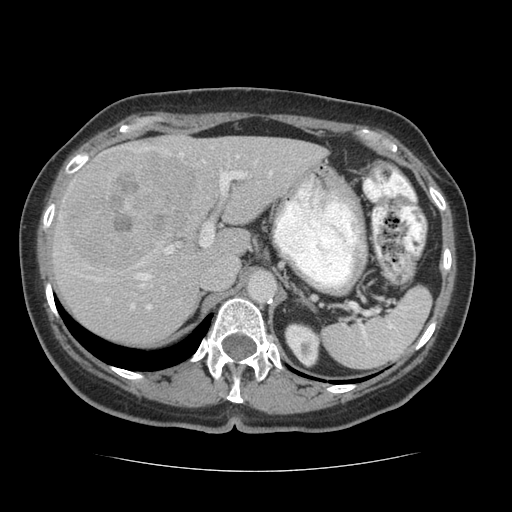
Contrast-enhanced abdominal CT (liver protocol), one axial slice; position 42 of 75 along the scan axis; 140 kVp; soft-tissue window (W 400 / L 40 HU); 2.5 mm slice thickness; 512 × 512 image matrix, field of view 360 × 360 mm. Case-level facts recorded for this patient, not image findings: diagnosis: hepatocellular carcinoma (patient treated with transarterial chemoembolisation; whether this scan precedes or follows treatment is not stated here); TNM stage (as recorded): Stage-I; Child-Pugh class: A; tumour differentiation: moderately differentiated; tumour nodularity: uninodular.
Structures marked on this image (semi-automatically segmented with operator editing):
- liver parenchyma outside the tumour (the mass and vessels are separate outlines, so this box may not span the whole liver): box from (x=52, y=134) to (x=326, y=344) px
- mass: (x=60, y=147)–(x=196, y=270)
- liver vessels: (x=60, y=147)–(x=273, y=310)